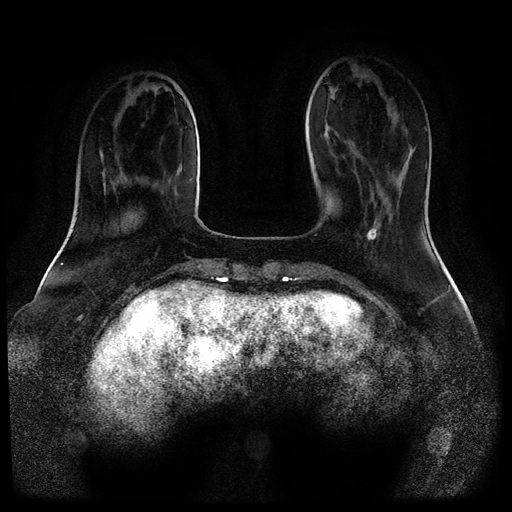
Breast MRI (dynamic contrast-enhanced, multi-phase), one axial slice; position 28 of 116 along the scan axis; dynamic contrast-enhanced series, time point 2 of 5 at this slice position (early post-contrast); 1.5 T; TE 2.6 ms, TR 5.3 ms; 2 mm slice thickness; 512 × 512 image matrix. Female patient, age 52 years.
Annotated regions visible in this slice (semi-automatic segmentation, software-assisted and operator-edited):
- breast lesion (labelled 'tumour' in the annotation; benign lesions carry a separate 'benign' label): bounding box (x1, y1, x2, y2) in pixels: (366, 219, 379, 241)